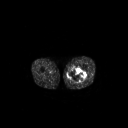
FDG PET of an extremity soft-tissue mass (from a PET/CT study), one axial slice. Position 239 of 267 along the scan axis. 128 × 128 image matrix. Patient: male, 44 years. From the clinical record (not read from this slice): histological type: undifferentiated pleomorphic liposarcoma; grade: high; site of the primary tumour: left thigh.
Structures marked on this image (expert contour drawn on MRI and transferred to this co-registered scan by the dataset authors):
- gross tumour volume including surrounding oedema: bounding box <67,68,86,83> (left, top, right, bottom; pixels)
- gross tumour volume (mass): <67,68,86,83>